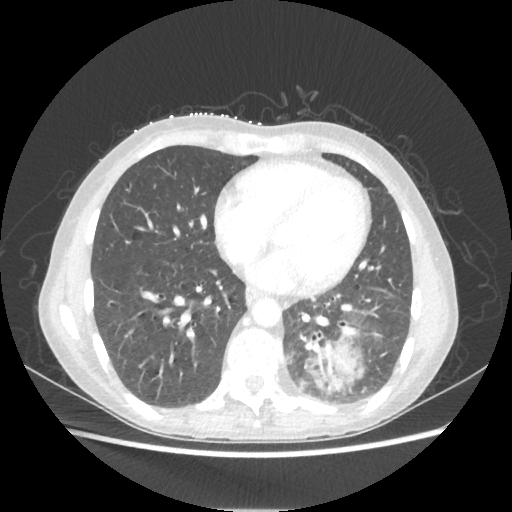
Chest CT, one axial slice. Position 85 of 221 along the scan axis. Reconstruction kernel STANDARD. Lung window (W 1500 / L -600 HU). 1.25 mm slice thickness. 512 × 512 image matrix, field of view 360 × 360 mm. Patient: female, 53 years. From the clinical record (not read from this slice): clinical TNM (as recorded): T3 N0 M0.
Annotated regions visible in this slice (bounding box drawn by a radiologist):
- lung tumour (recorded histology: adenocarcinoma): box from (x=304, y=341) to (x=363, y=393) px